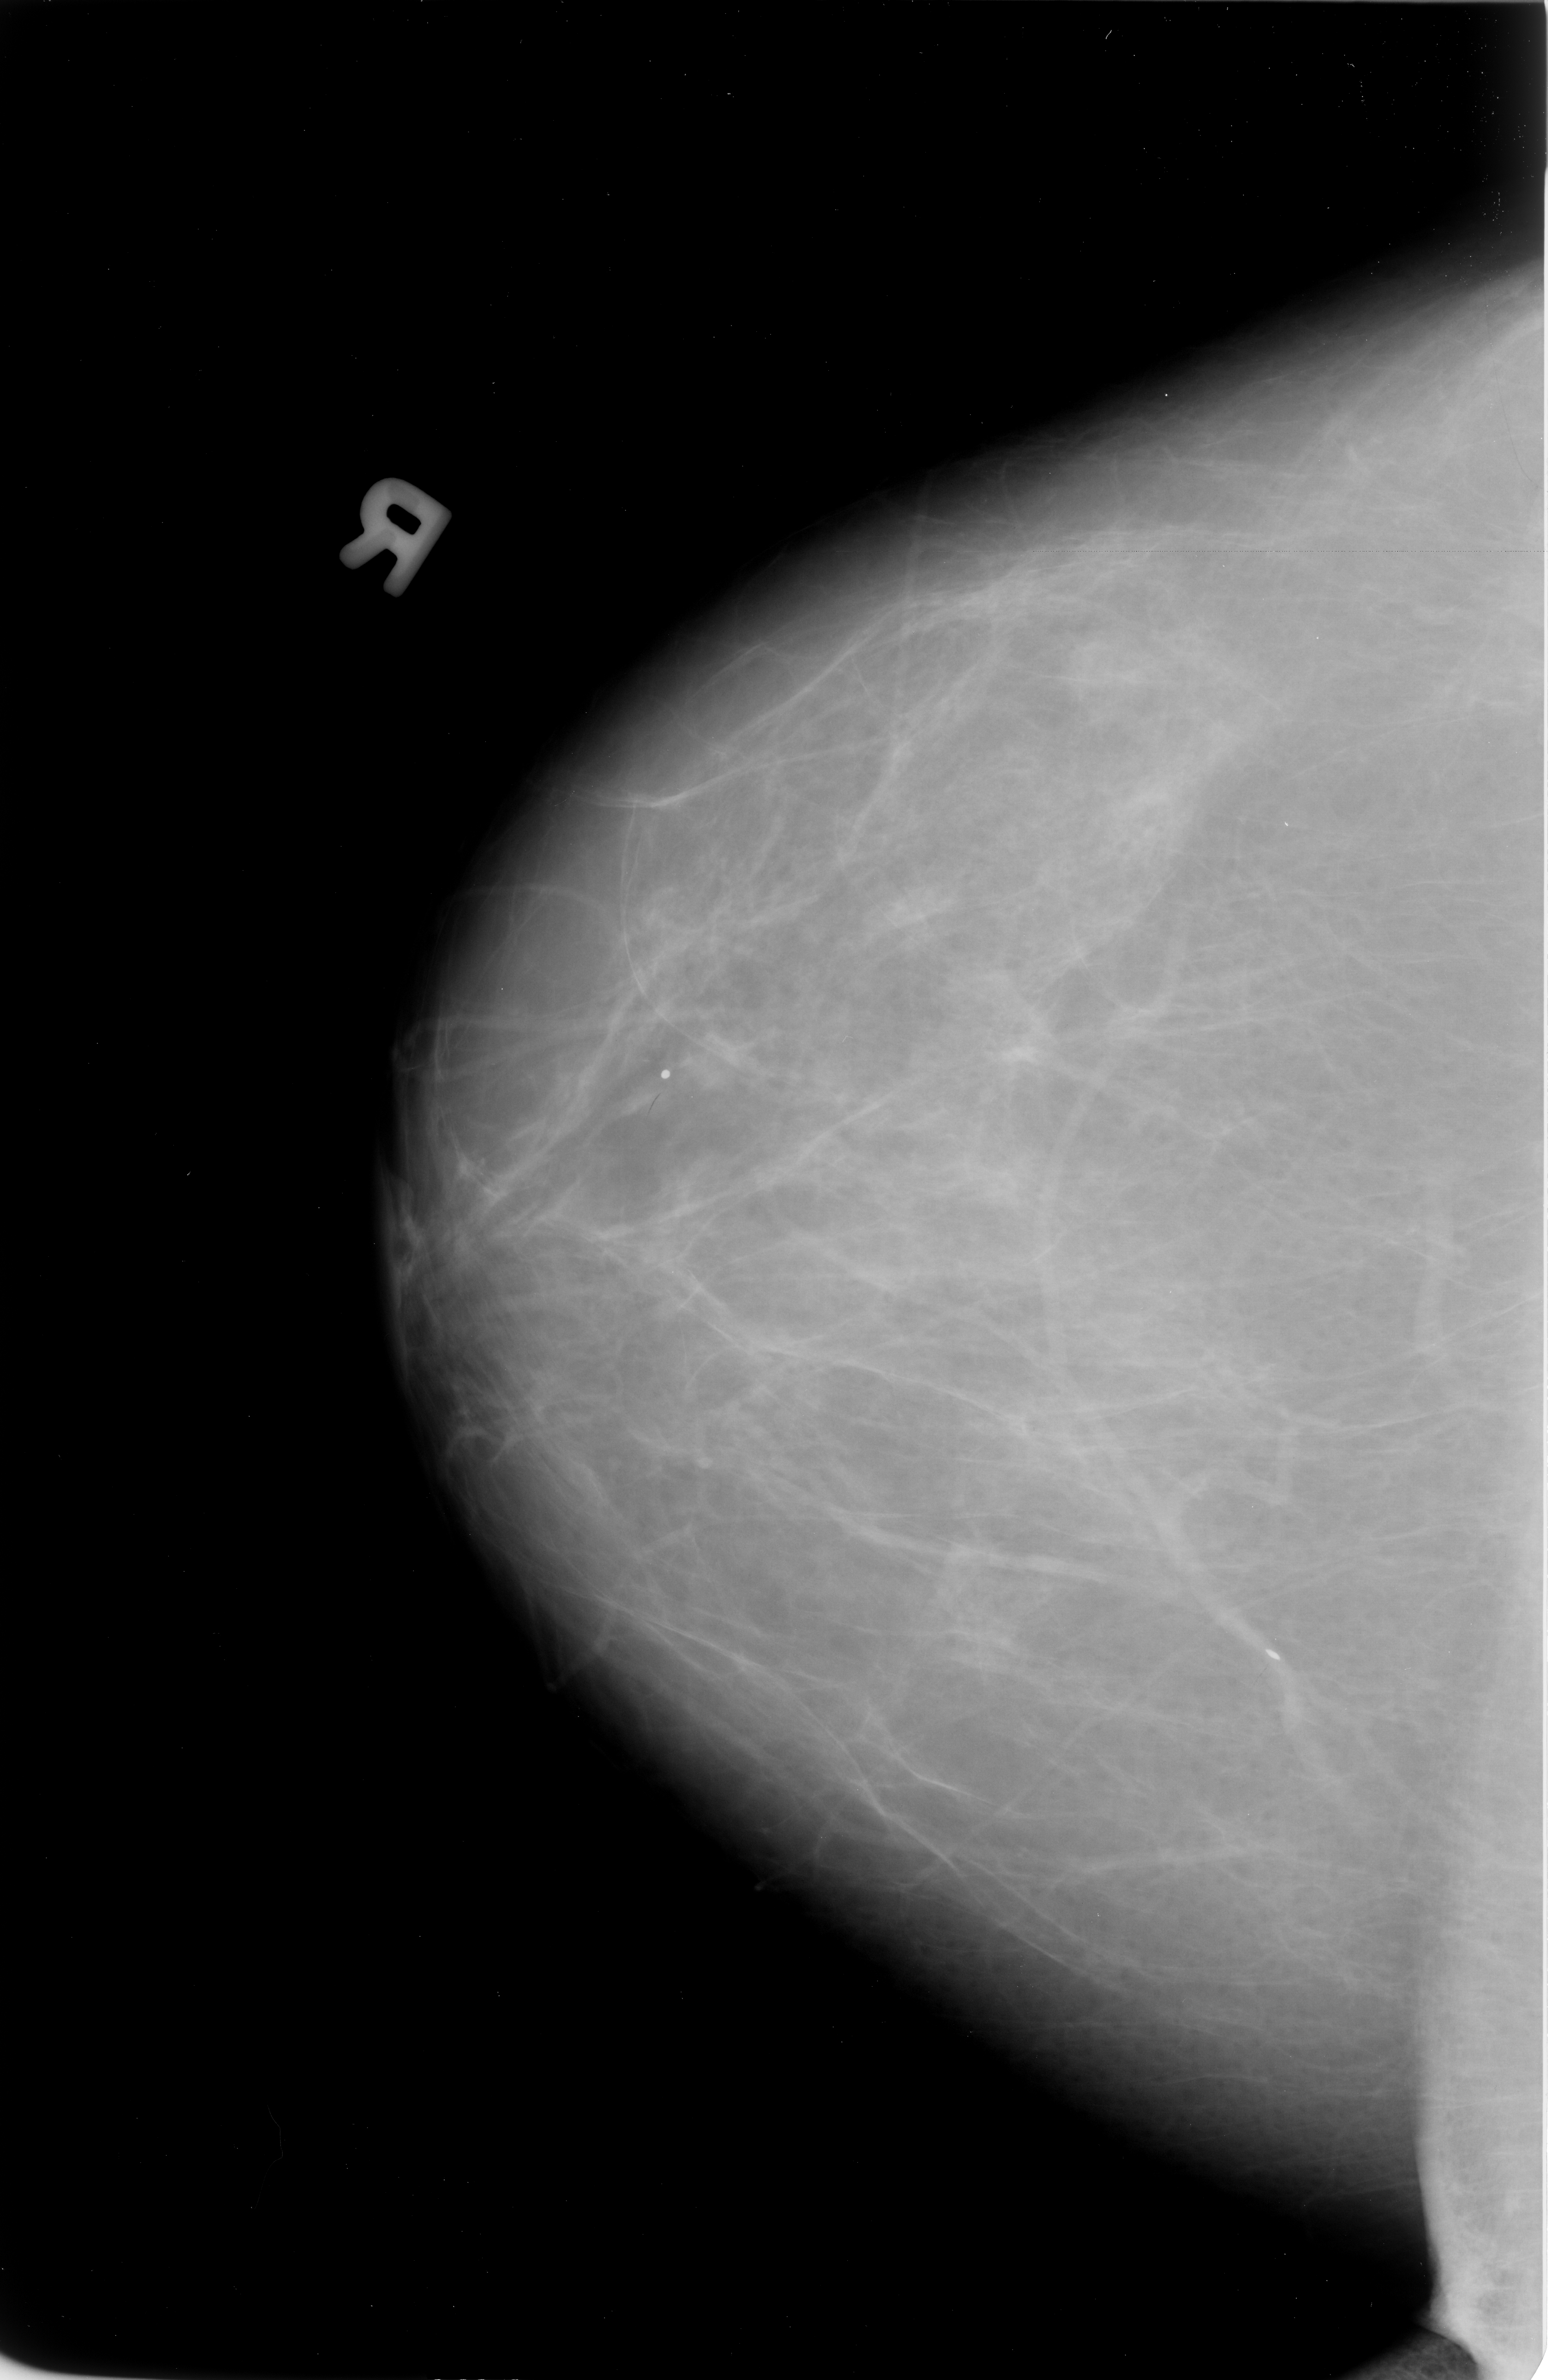
Mammogram (digitized film); right breast; CC view; breast composition: almost entirely fatty (BI-RADS density category 1 of 4); 1548 × 2380 image matrix.
Expert-marked regions of interest on this image (one box per marked abnormality):
- Finding 1 of 2: calcifications, morphology coarse; BI-RADS assessment category 2; subtlety rating 3 on a 1 (subtle) to 5 (obvious) scale; outcome (as recorded, no biopsy): benign without callback (not worked up further): bounding box <636,1044,710,1131> (left, top, right, bottom; pixels)
- Finding 2 of 2: calcifications, morphology vascular; BI-RADS assessment category 2; subtlety rating 3 on a 1 (subtle) to 5 (obvious) scale; outcome (as recorded, no biopsy): benign without callback (not worked up further): <1239,1630,1324,1688>